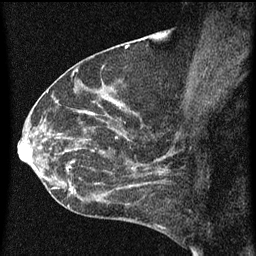
Breast MRI (dynamic contrast-enhanced), one sagittal slice. Slice 34 of 60 in the series (ordered by position). Dynamic contrast-enhanced series, image 2 of 3 at this slice position (ordered by acquisition). 1.5 T. TE 4.2 ms, TR 8 ms. 256 × 256 image matrix. Patient: female, 54 years.
Annotated regions visible in this slice (semi-automatic segmentation, software-assisted and operator-edited):
- analysis volume of interest (the breast-tissue region the enhancement analysis was run in; not a lesion): box from (x=49, y=138) to (x=164, y=209) px
- tumour enhancement mask (voxels above the 70 % enhancement threshold inside the analysis volume of interest): (x=52, y=138)–(x=164, y=207)